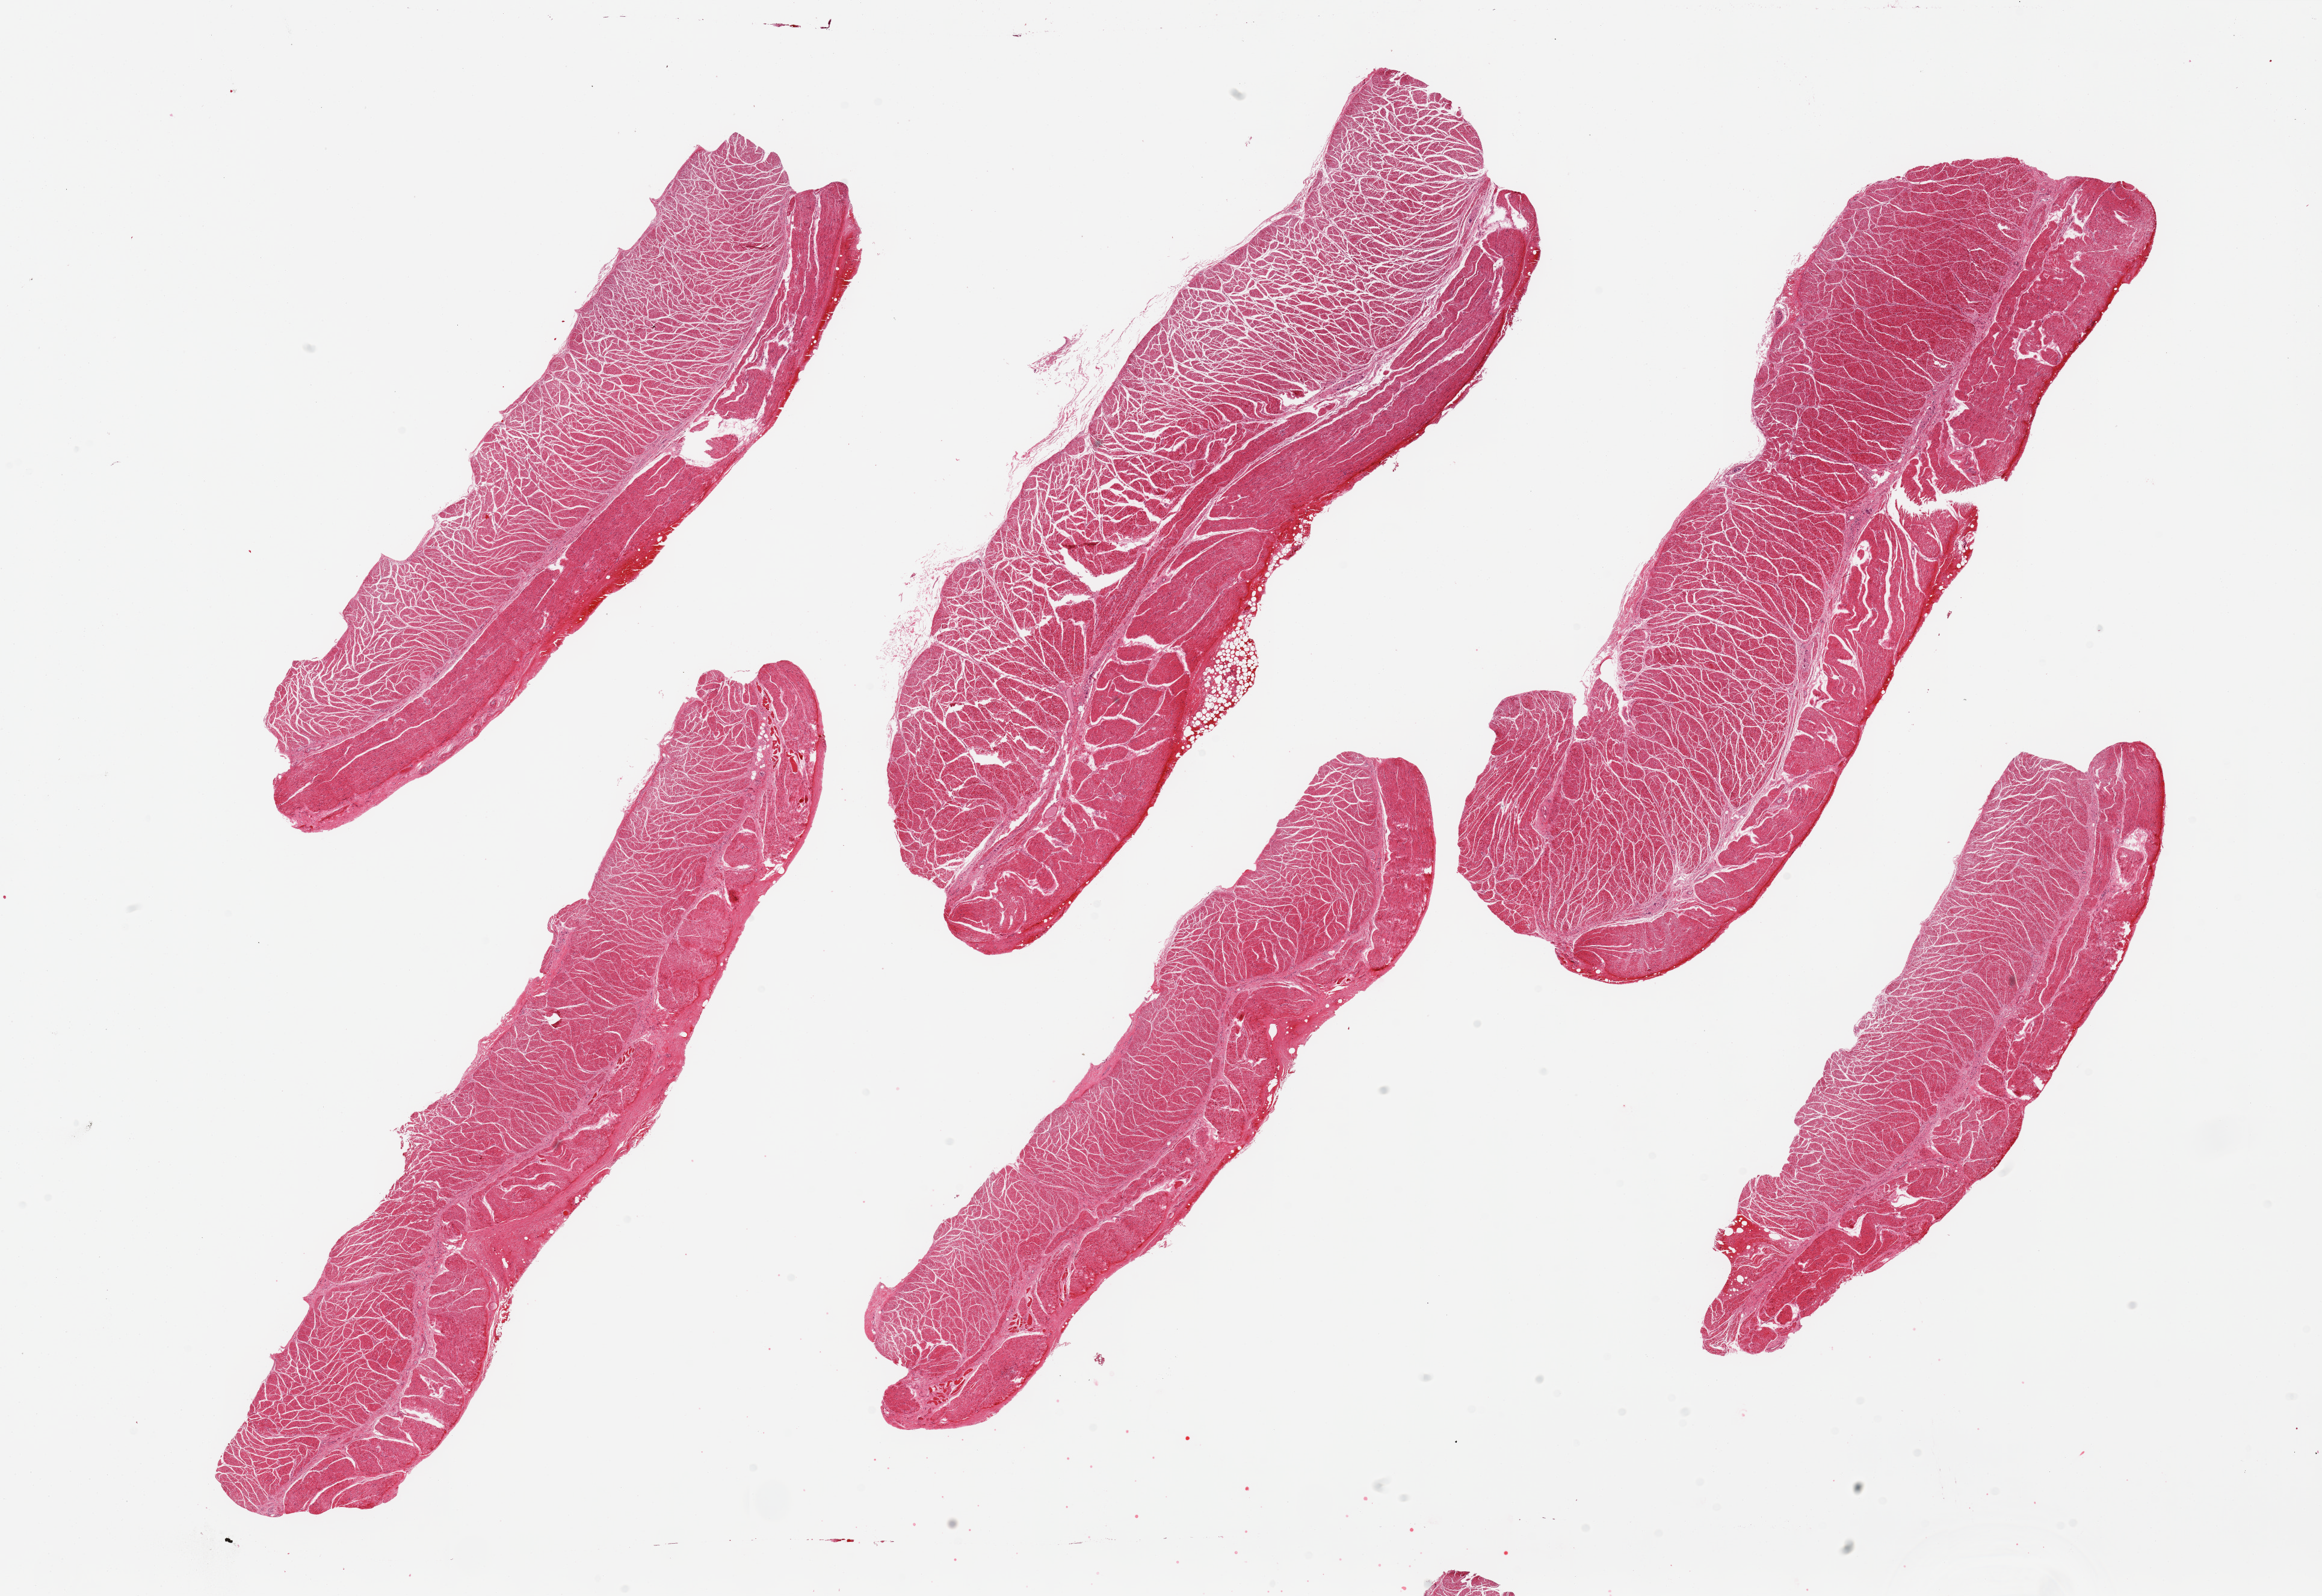
Whole-slide image, hematoxylin and eosin (H&E) stain — shown as a low-resolution overview of the whole scanned area (about 30.5 x 21.0 mm, slide scanned at 20x); PAXgene-fixed paraffin-embedded (PFPE) section; section of esophageal muscle (target tissue); tissue donor sample. Male donor.
Pathologist's review note for this sample: 6 pieces; well trimmed muscularis.